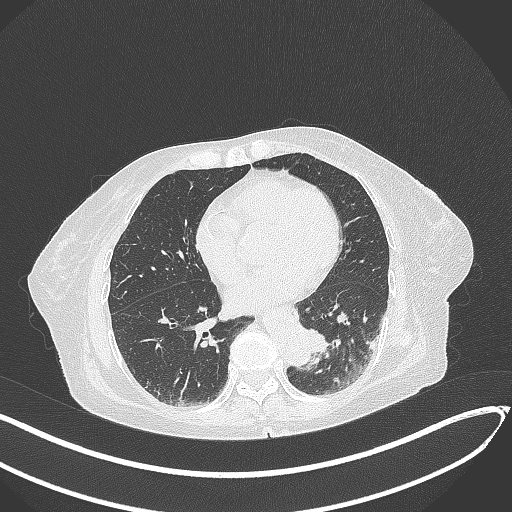
Chest CT, one axial slice. Slice 89 of 324 in the series (ordered by position). Reconstruction kernel B70f. 120 kVp. Lung window (W 1500 / L -600 HU). 1 mm slice thickness. 512 × 512 image matrix, field of view 400 × 400 mm. Female patient, age 82 years. Case-level facts recorded for this patient, not image findings: clinical TNM (as recorded): T1b N0 M1.
Annotated regions visible in this slice (bounding box drawn by a radiologist):
- lung tumour (recorded histology: adenocarcinoma): bounding box [x1, y1, x2, y2] px = [301, 323, 333, 361]